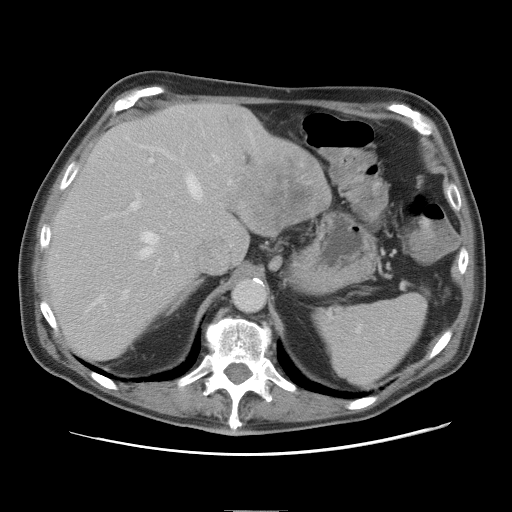
Contrast-enhanced abdominal CT, one axial slice. Slice 56 of 89 in the series (ordered by position). 120 kVp. Intravenous contrast given. Soft-tissue window (W 400 / L 40 HU). 512 × 512 image matrix. Male patient, age 69 years. Case-level facts recorded for this patient, not image findings: diagnosis: colorectal cancer liver metastases, imaged before liver resection; multiple liver metastases: no; largest metastasis: 8.5 cm.
Annotated regions visible in this slice (outlined manually by an expert reader):
- hepatic veins: bounding box <96,170,204,302> (left, top, right, bottom; pixels)
- liver: <48,103,329,359>
- planned liver remnant (the part of the liver to remain after resection): <49,103,247,359>
- portal vein (with intrahepatic branches): <125,153,231,296>
- liver metastasis: <242,160,318,234>